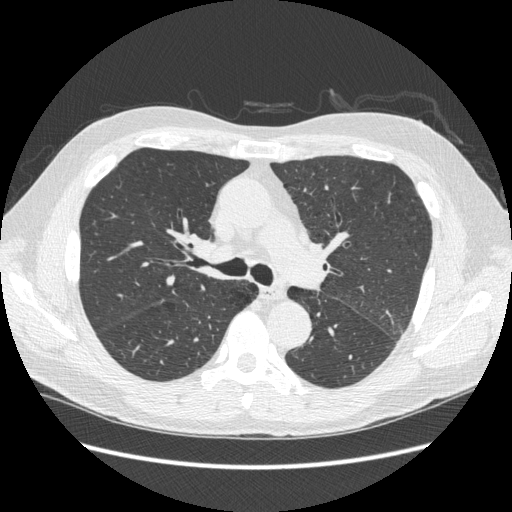
Axial slice from a low-dose chest CT screening exam. Third annual screen. Lung window (W 1500 / L -600 HU). 1.25 mm slice thickness. Standard (soft-tissue) reconstruction kernel (STANDARD). Slice 102 of 258 in the series. Male, age 59 years at enrolment. Current smoker at enrolment.
Expert reader's lesion annotation, bounding box (x1, y1, x2, y2) in pixels: (176, 225, 226, 271). The screening reader recorded 2 non-calcified nodules or masses ≥4 mm on this exam (right upper lobe, left lower lobe); which of them this box marks is not recorded. Lung cancer was diagnosed 169 days after this screen: squamous cell carcinoma, keratinizing, NOS, right hilum, stage IIIB (AJCC 6th edition).